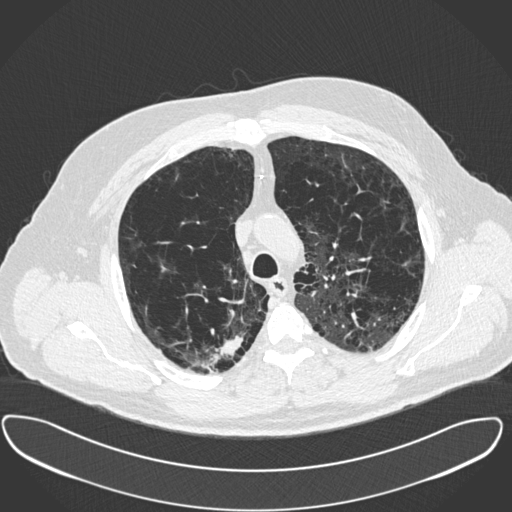
Low-dose screening chest CT, one axial slice; slice 294 of 385 in the series (ordered by position); lung window (W 1500 / L -600 HU); 1 mm slice thickness; 512 × 512 image matrix, field of view 408 × 408 mm.
Outlined on this slice (outlined manually by an expert reader):
- lesion 1 (tumor, upper lobe of right lung): box from (x=194, y=336) to (x=243, y=372) px